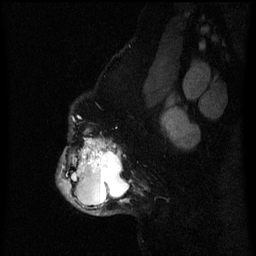
Breast MRI (dynamic contrast-enhanced), one sagittal slice; position 50 of 60 along the scan axis; dynamic contrast-enhanced series, image 2 of 3 at this slice position (ordered by acquisition); 1.5 T; TE 4.2 ms, TR 8 ms; 2 mm slice thickness; 256 × 256 image matrix. Female patient, age 50 years.
Structures marked on this image (semi-automatic segmentation, software-assisted and operator-edited):
- analysis volume of interest (the breast-tissue region the enhancement analysis was run in; not a lesion): bounding box <56,132,130,216> (left, top, right, bottom; pixels)
- tumour enhancement mask (voxels above the 70 % enhancement threshold inside the analysis volume of interest): <59,139,129,215>